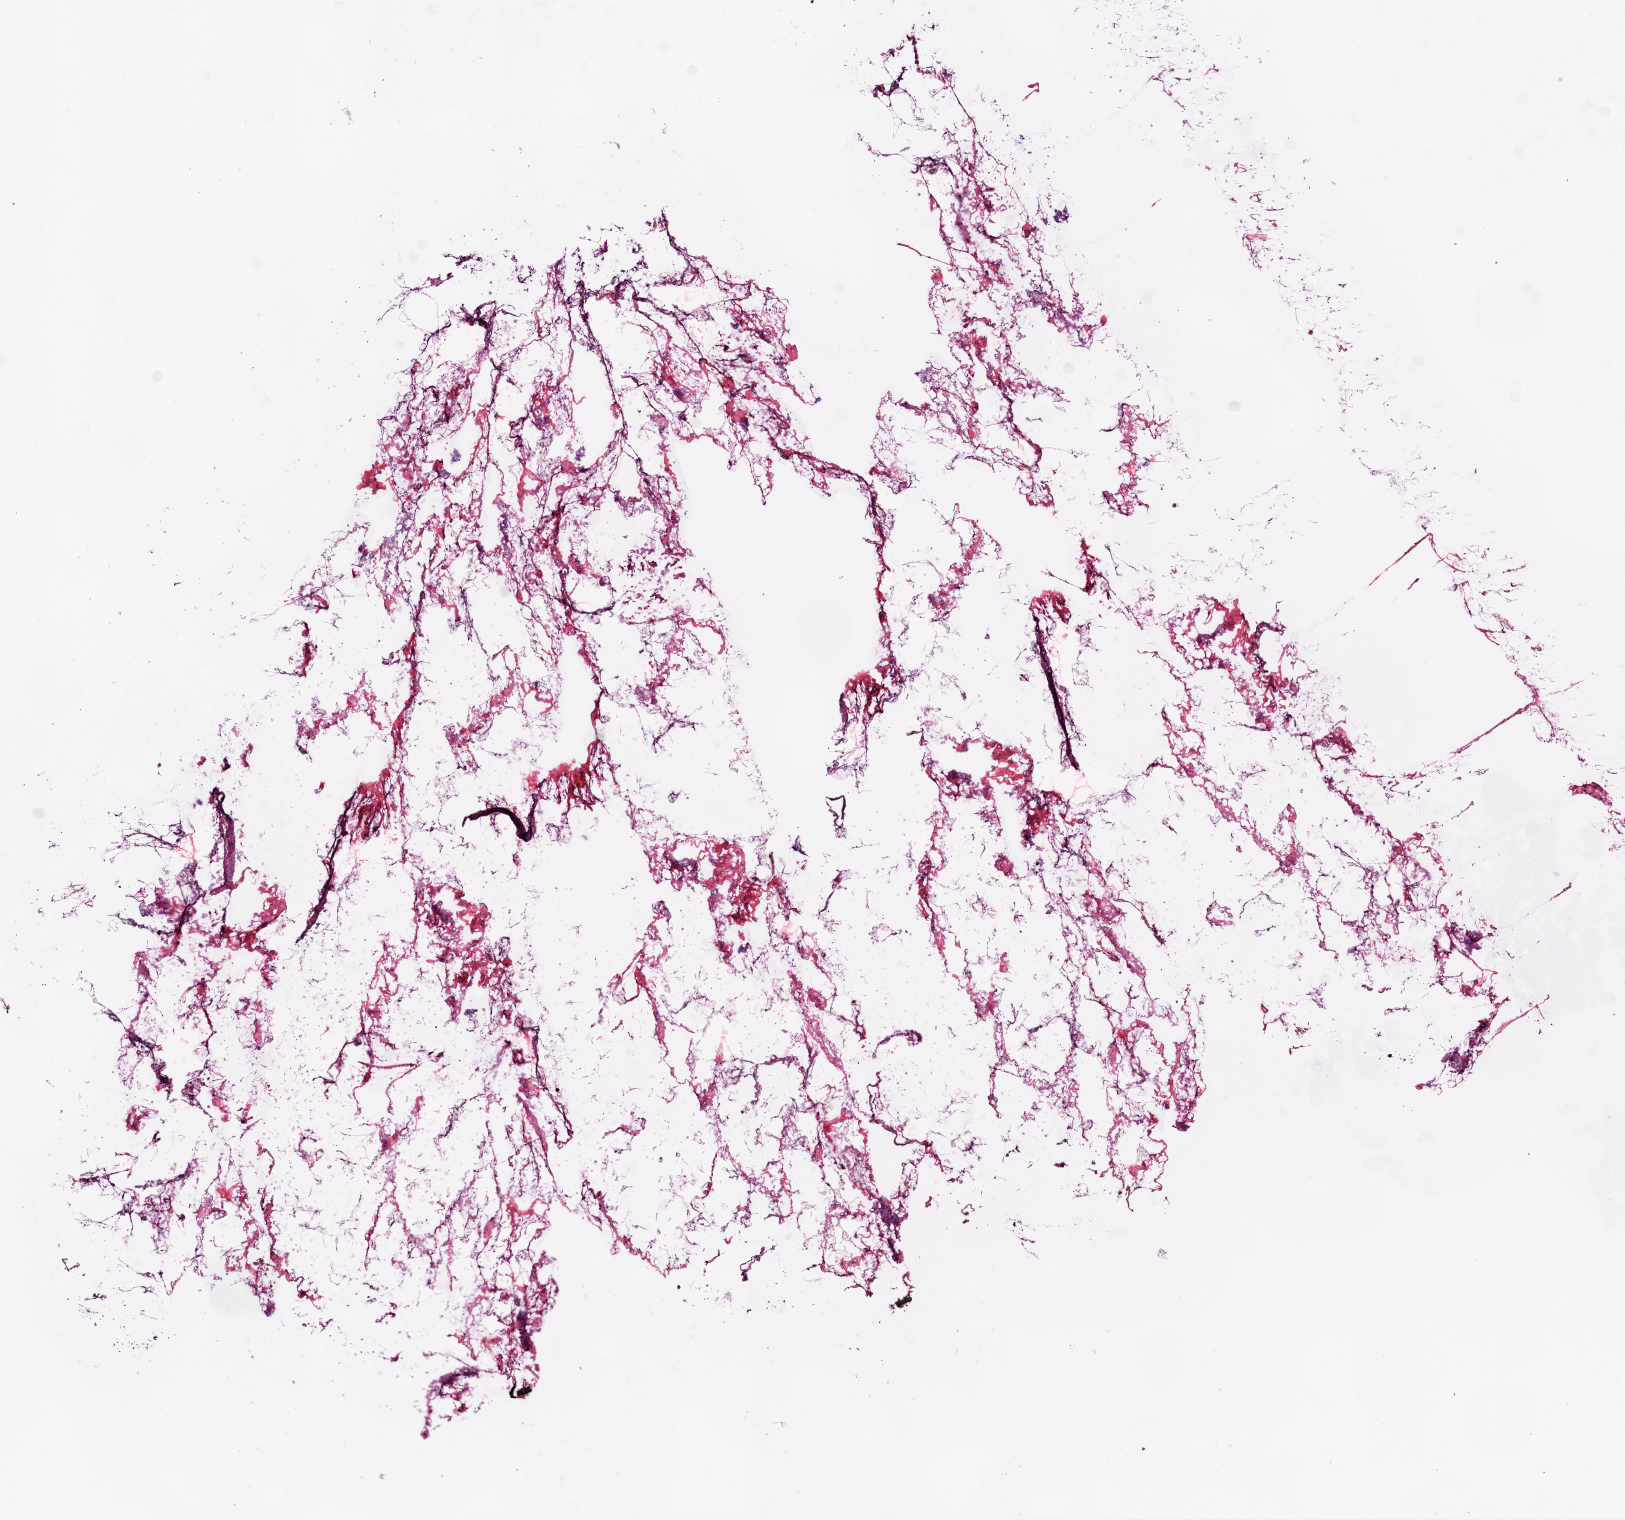
Digitized H&E-stained tissue section (whole slide), a low-resolution overview of the entire scanned area, about 13.0 x 12.2 mm; frozen section; sample: solid tissue normal (non-tumour tissue), ovary. Patient: female, age at initial diagnosis 57 years.
• this section: solid tissue normal (non-tumour) sample from the same patient
• patient diagnosis: Serous cystadenocarcinoma, NOS